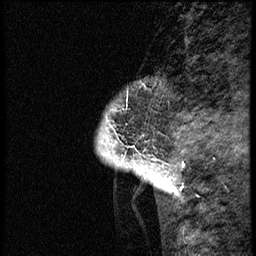
Breast MRI (dynamic contrast-enhanced), one sagittal slice; position 2 of 68 along the scan axis; dynamic contrast-enhanced study with each time point stored as its own series, time point 2 of 3 at this slice position (early post-contrast, ordered by acquisition time); 1.5 T; TE 4.2 ms, TR 17.6 ms; 256 × 256 image matrix. Patient: female, 52 years. From the clinical record (not read from this slice): setting: breast cancer imaged before/during neoadjuvant chemotherapy; receptor status: HER2-positive.
Annotated regions visible in this slice (semi-automatically segmented with operator editing):
- analysis volume of interest (the breast-tissue region the enhancement analysis was run in; not a lesion): bounding box <96,79,176,184> (left, top, right, bottom; pixels)
- tumour enhancement mask (voxels above the 100 % enhancement threshold inside the analysis volume of interest): <105,119,176,167>